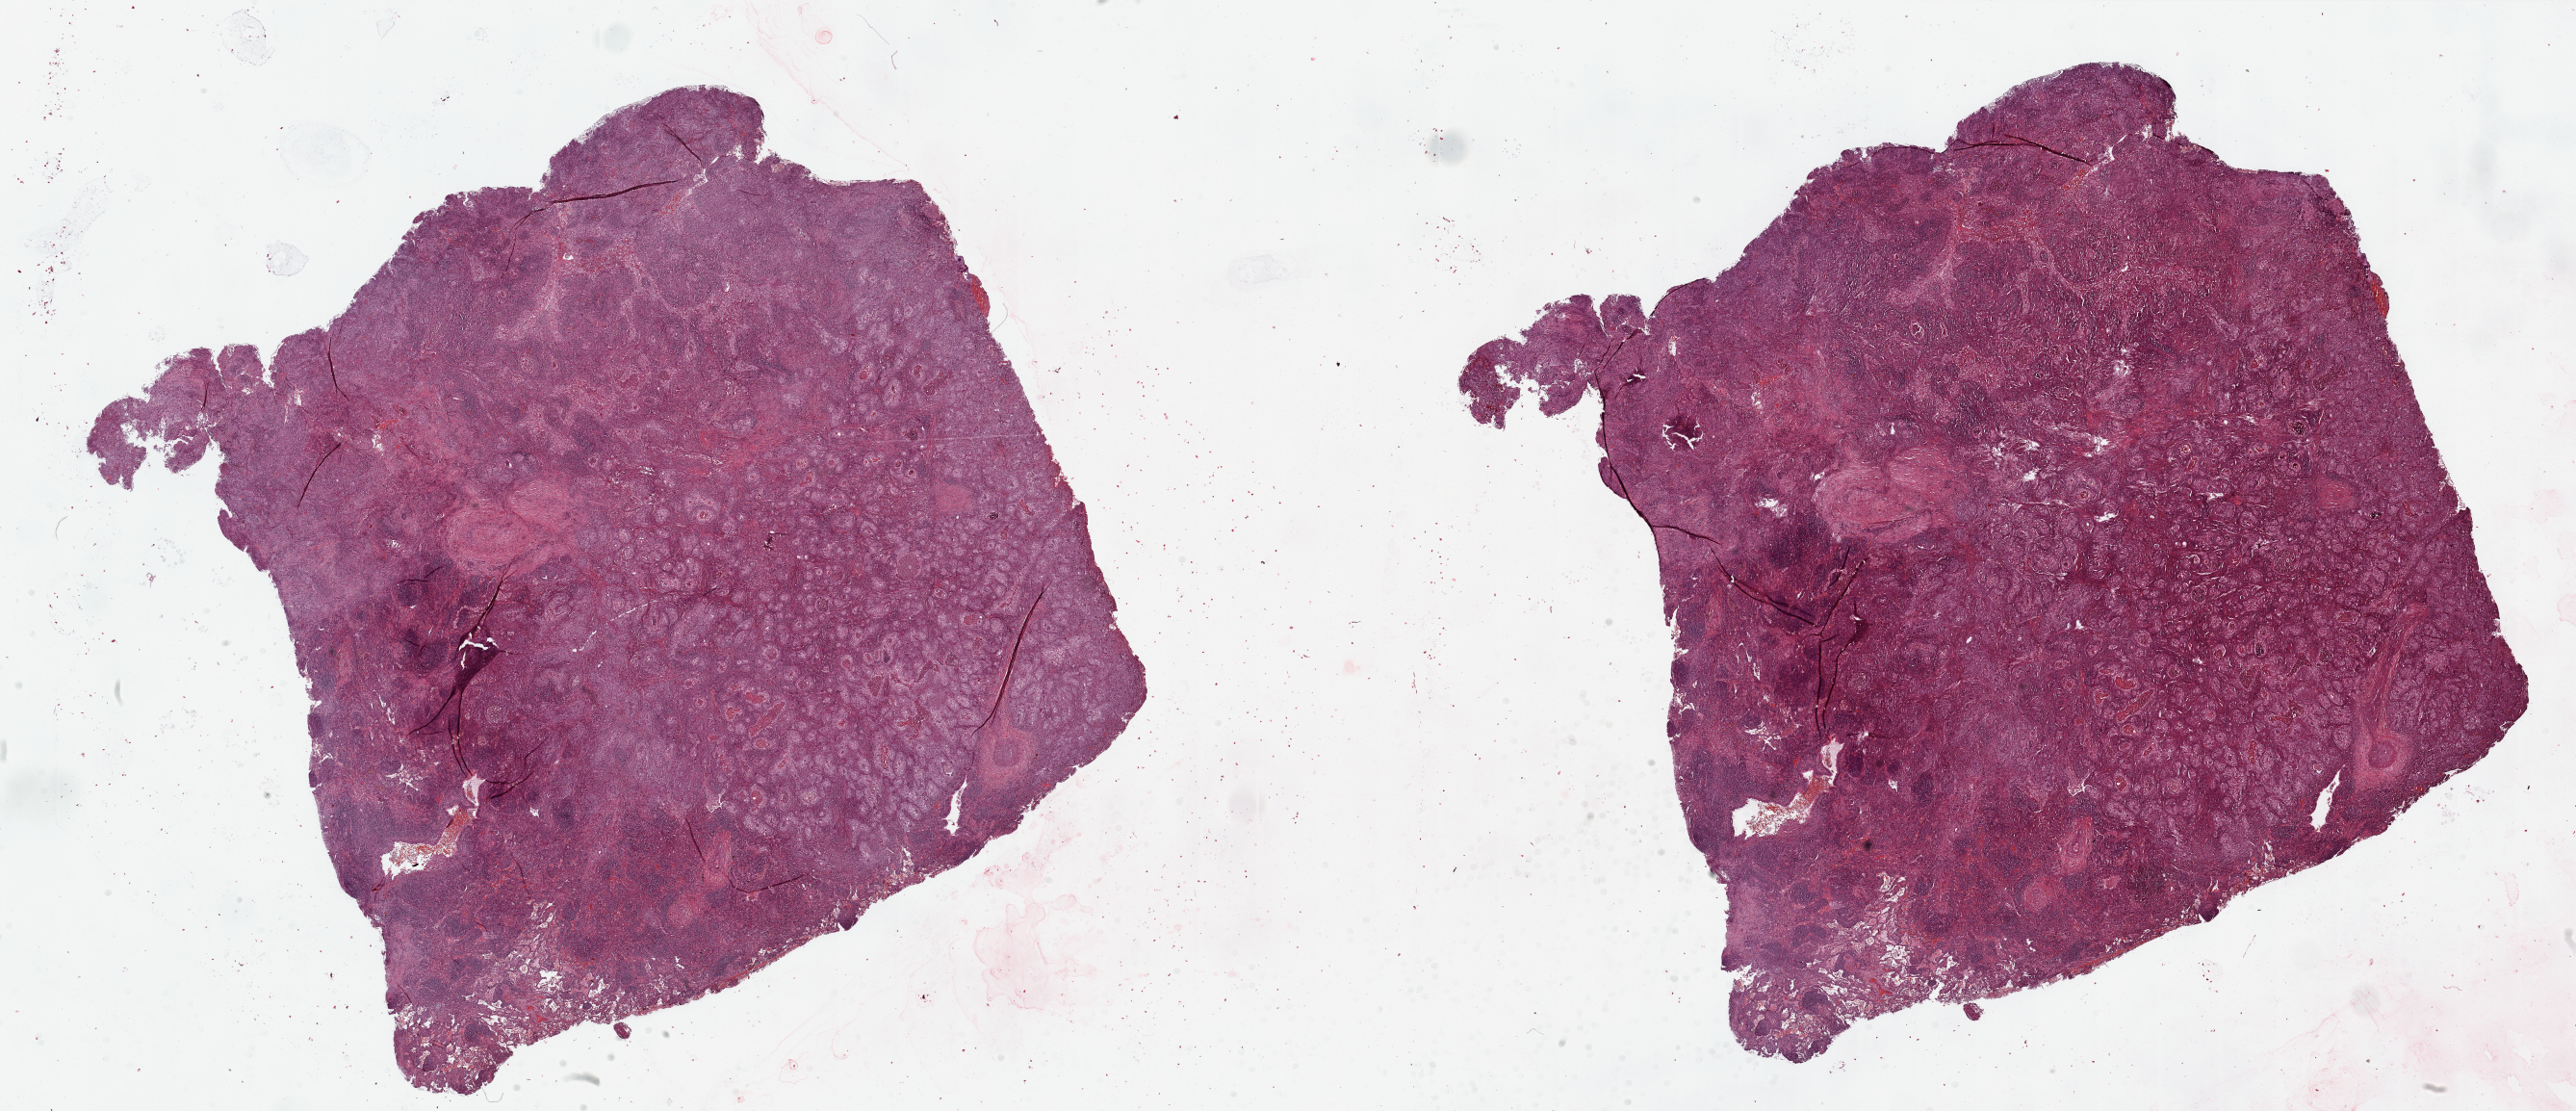
Digitized H&E-stained tissue section (whole slide) — shown as a low-resolution overview of the whole scanned area (about 42.3 x 18.3 mm). Tumour tissue sample, sampled site: lung. 73-year-old male patient. Histologic grade: G2 (moderately differentiated). Composition of this section per pathologist review: tumour nuclei 75%, necrosis 5%.
* histologic diagnosis: Squamous cell carcinoma, NOS
* AJCC pathologic stage: IB
* primary tumour site (as recorded): right lower lobe